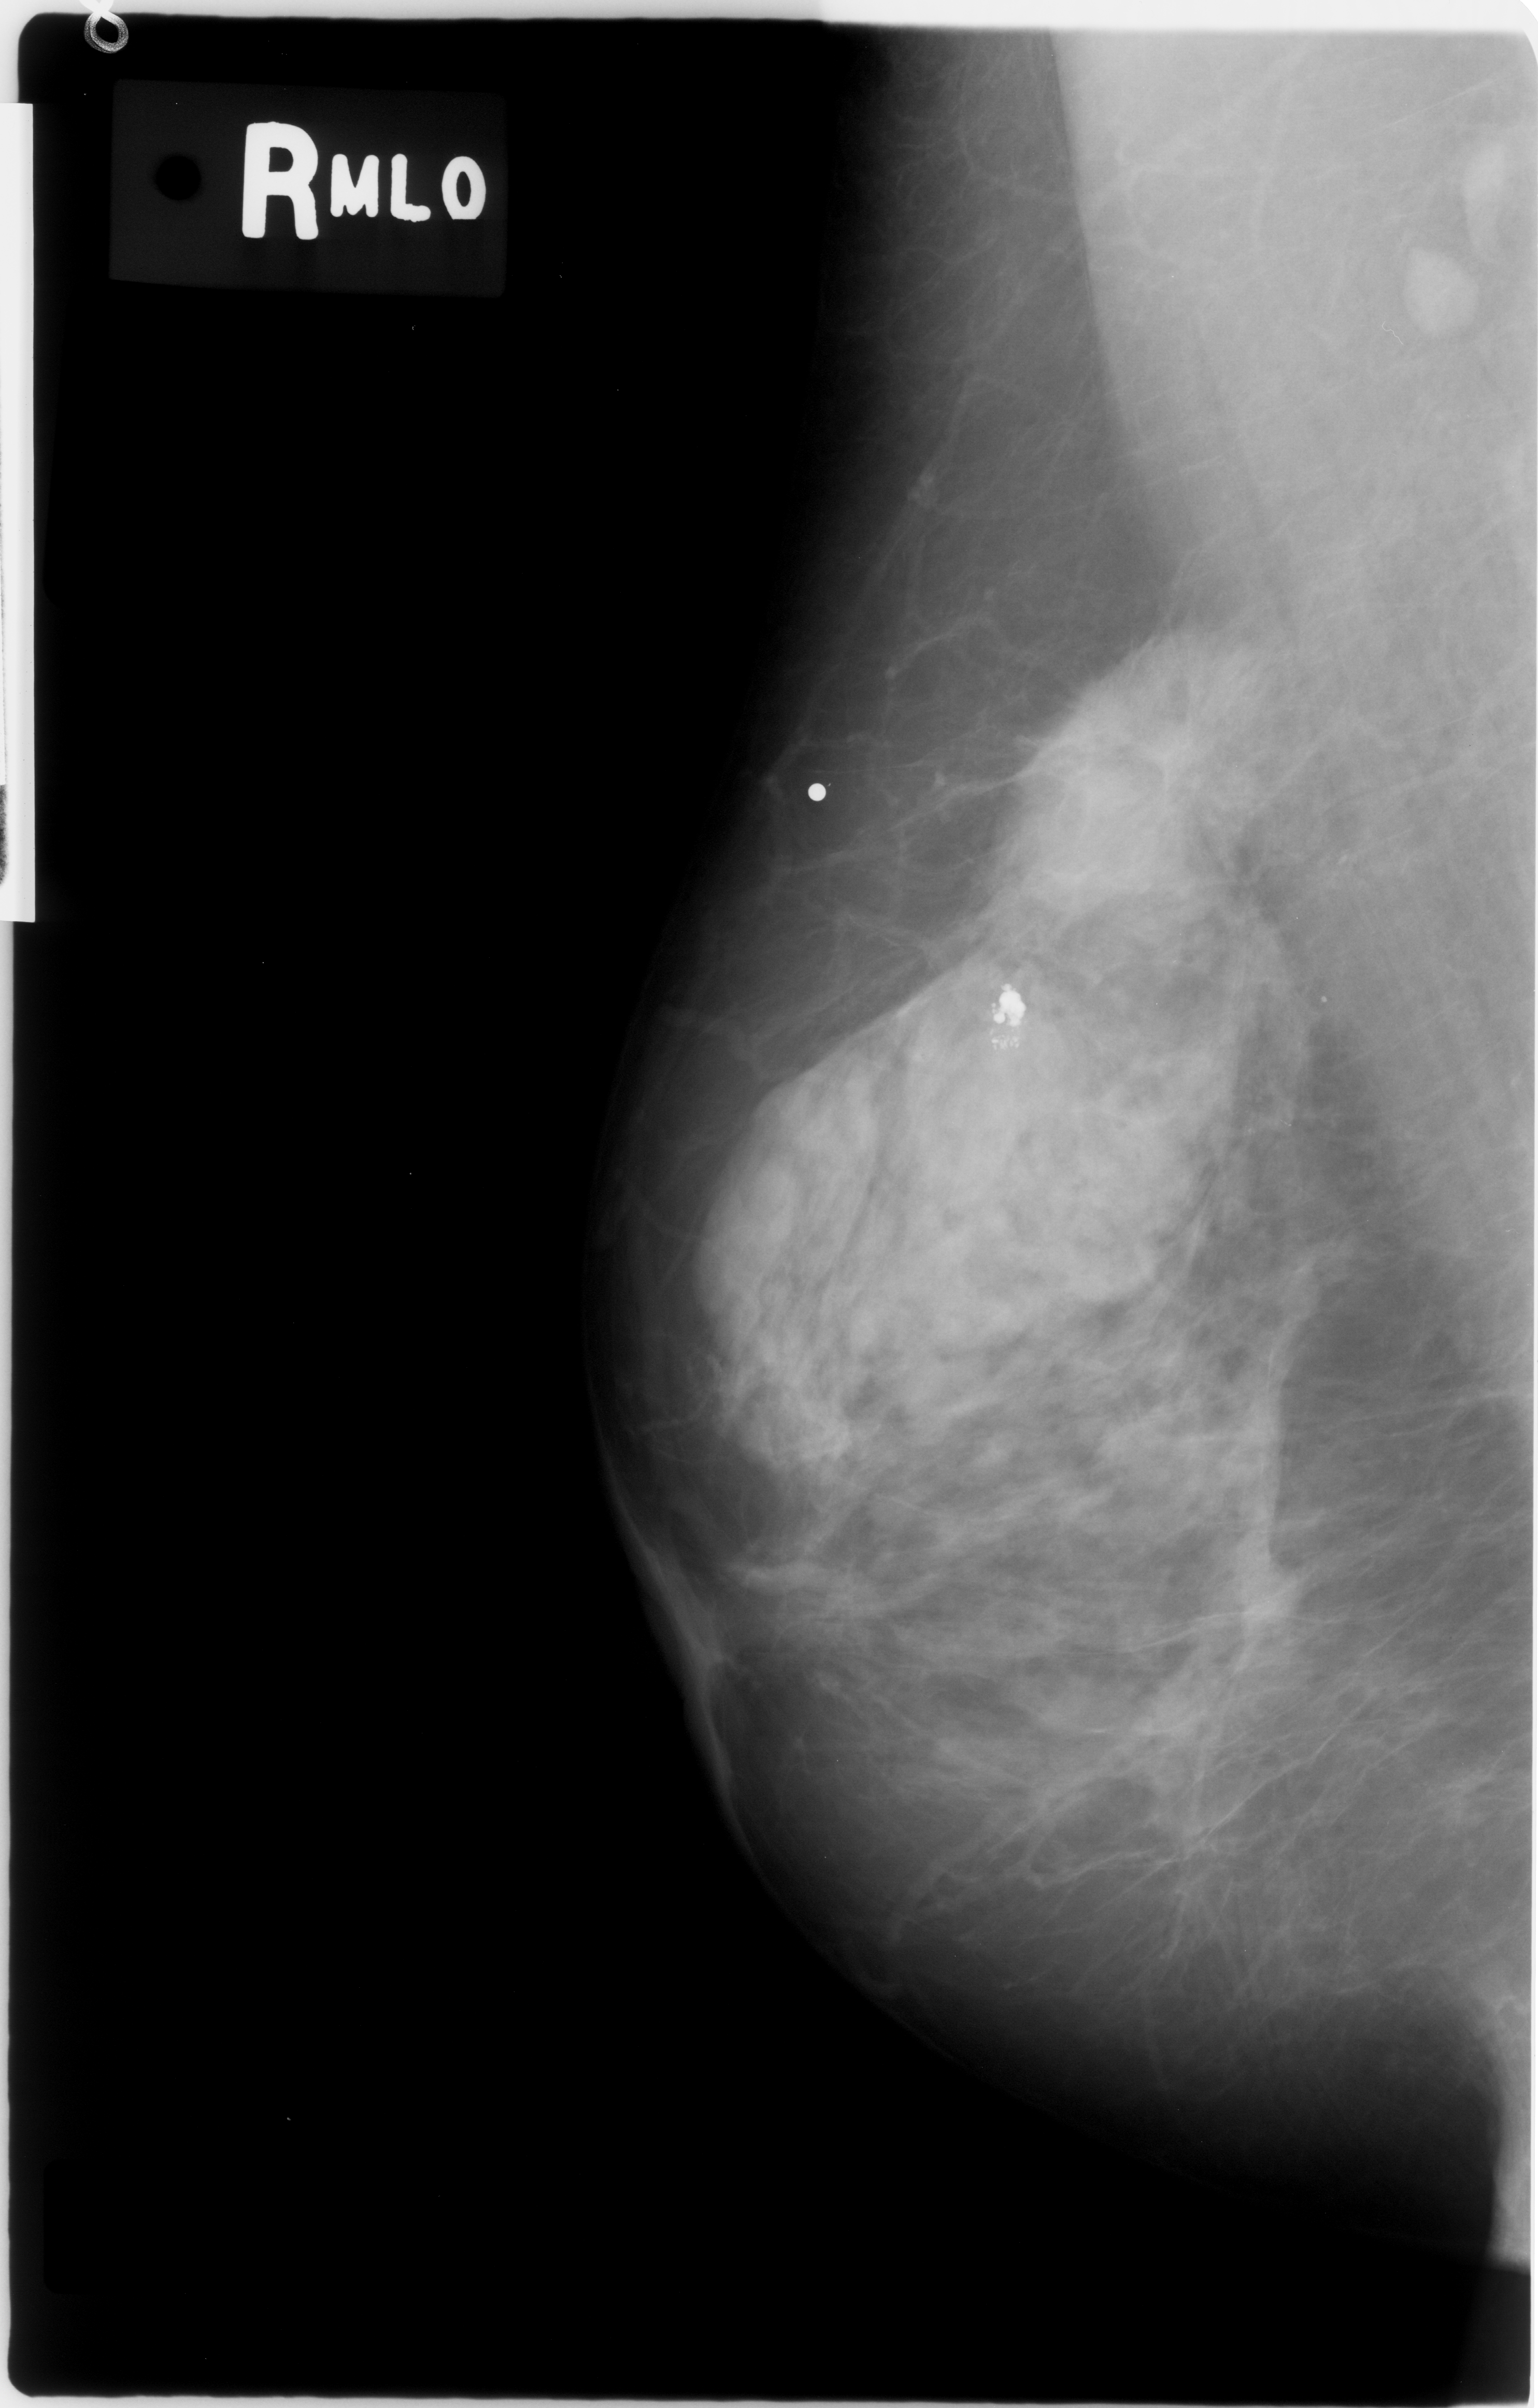
Mammogram (digitized film); right breast; mediolateral oblique (MLO) view; breast composition: heterogeneously dense (BI-RADS density category 3 of 4); 1538 × 2408 image matrix.
Marked abnormalities (boxes around the expert regions of interest):
- mass, shape irregular, margins spiculated; BI-RADS assessment category 5; pathology result (as recorded, not read from the image): malignant: bounding box [x1, y1, x2, y2] px = [984, 653, 1247, 897]